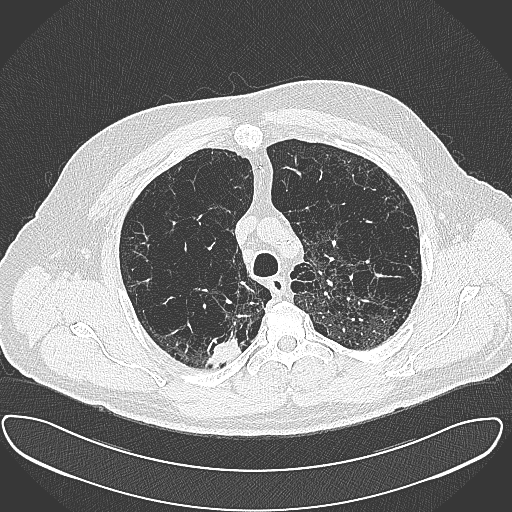
Axial slice from a low-dose chest CT screening exam. First (baseline) screen. Lung window (W 1500 / L -600 HU). 1 mm slice thickness. 120 kVp. Male, age 60 years at enrolment. Current smoker at enrolment.
- Expert reader's lesion annotation, bounding box [x1, y1, x2, y2] px = [198, 327, 245, 369].
- Reader record for this screening exam (exam-level; its link to the box is not recorded): non-calcified nodule or mass ≥4 mm, right upper lobe, 15 × 25 mm, spiculated (stellate) margins, soft tissue attenuation.
- Lung cancer was diagnosed 32 days after this screen: carcinoma, NOS, right upper lobe, moderately differentiated (G2), stage IB (AJCC 6th edition), 35 mm at pathology.